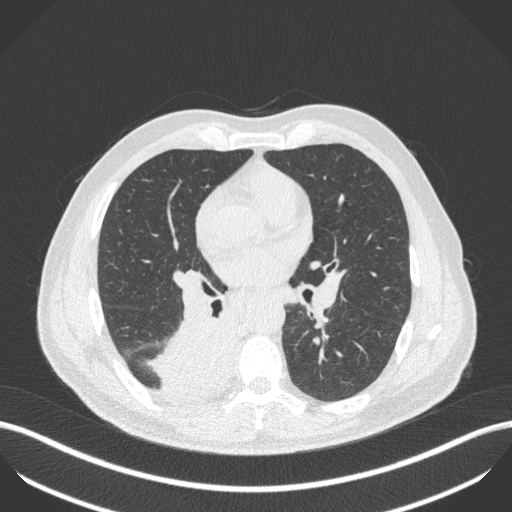
Chest CT, one axial slice; position 249 of 451 along the scan axis; reconstruction kernel B31f; lung window (W 1500 / L -600 HU); 512 × 512 image matrix, field of view 400 × 400 mm. Male patient, age 61 years. From the clinical record (not read from this slice): clinical TNM (as recorded): T1 N0 M0; histopathological grade: G3.
Outlined on this slice (bounding box drawn by a radiologist):
- lung tumour (recorded histology: small cell carcinoma): bounding box <147,313,243,396> (left, top, right, bottom; pixels)